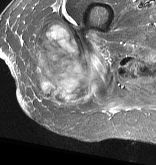
MRI of an extremity soft-tissue mass, one axial slice; position 18 of 57 along the scan axis; STIR; MR volume resampled by the dataset authors to the PET/CT grid (not the native acquisition matrix); 156 × 165 image matrix, field of view 152 × 161 mm. Female patient. From the clinical record (not read from this slice): histological type: epithelioid sarcoma with vascular differentiation; site of the primary tumour: right buttock.
Annotated regions visible in this slice (expert contour drawn on MRI and transferred to this co-registered scan by the dataset authors):
- gross tumour volume (mass): box from (x=29, y=21) to (x=109, y=109) px